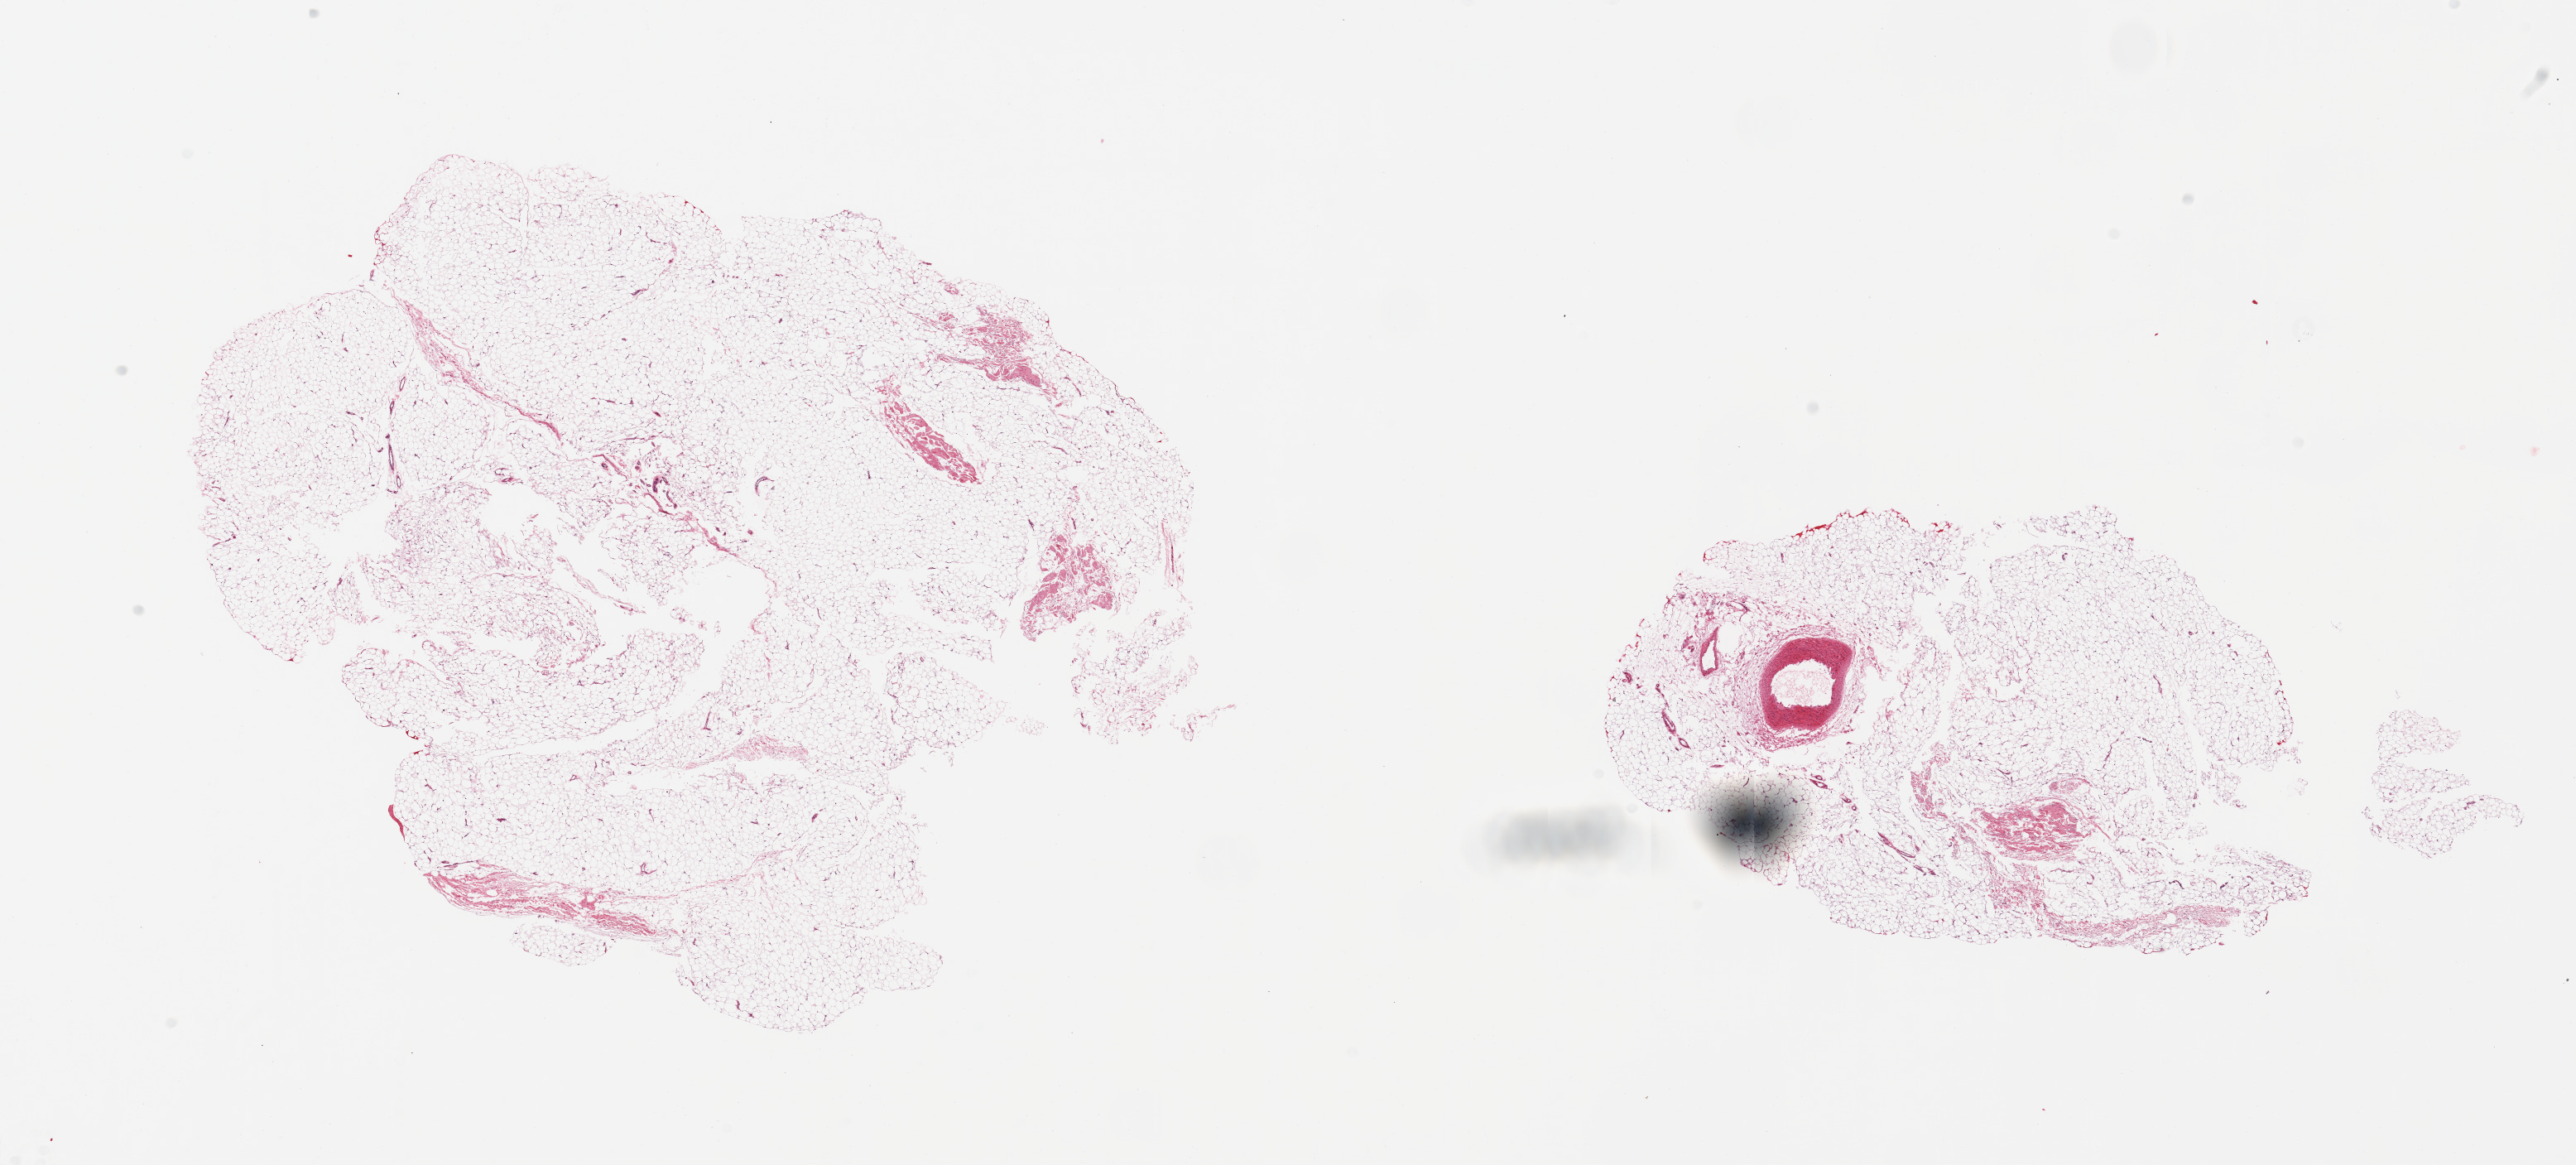
Haematoxylin and eosin whole-slide image — whole scanned area (about 24.6 x 11.1 mm, from a 20x scan) shown as a low-resolution overview. PAXgene-fixed, paraffin-embedded tissue. Section of adipose tissue (target tissue). Tissue donor sample. Donor sex: male.
• pathologist's review note for this sample: 2 pieces; adipose tissue with 1 mm artery in 1 piece